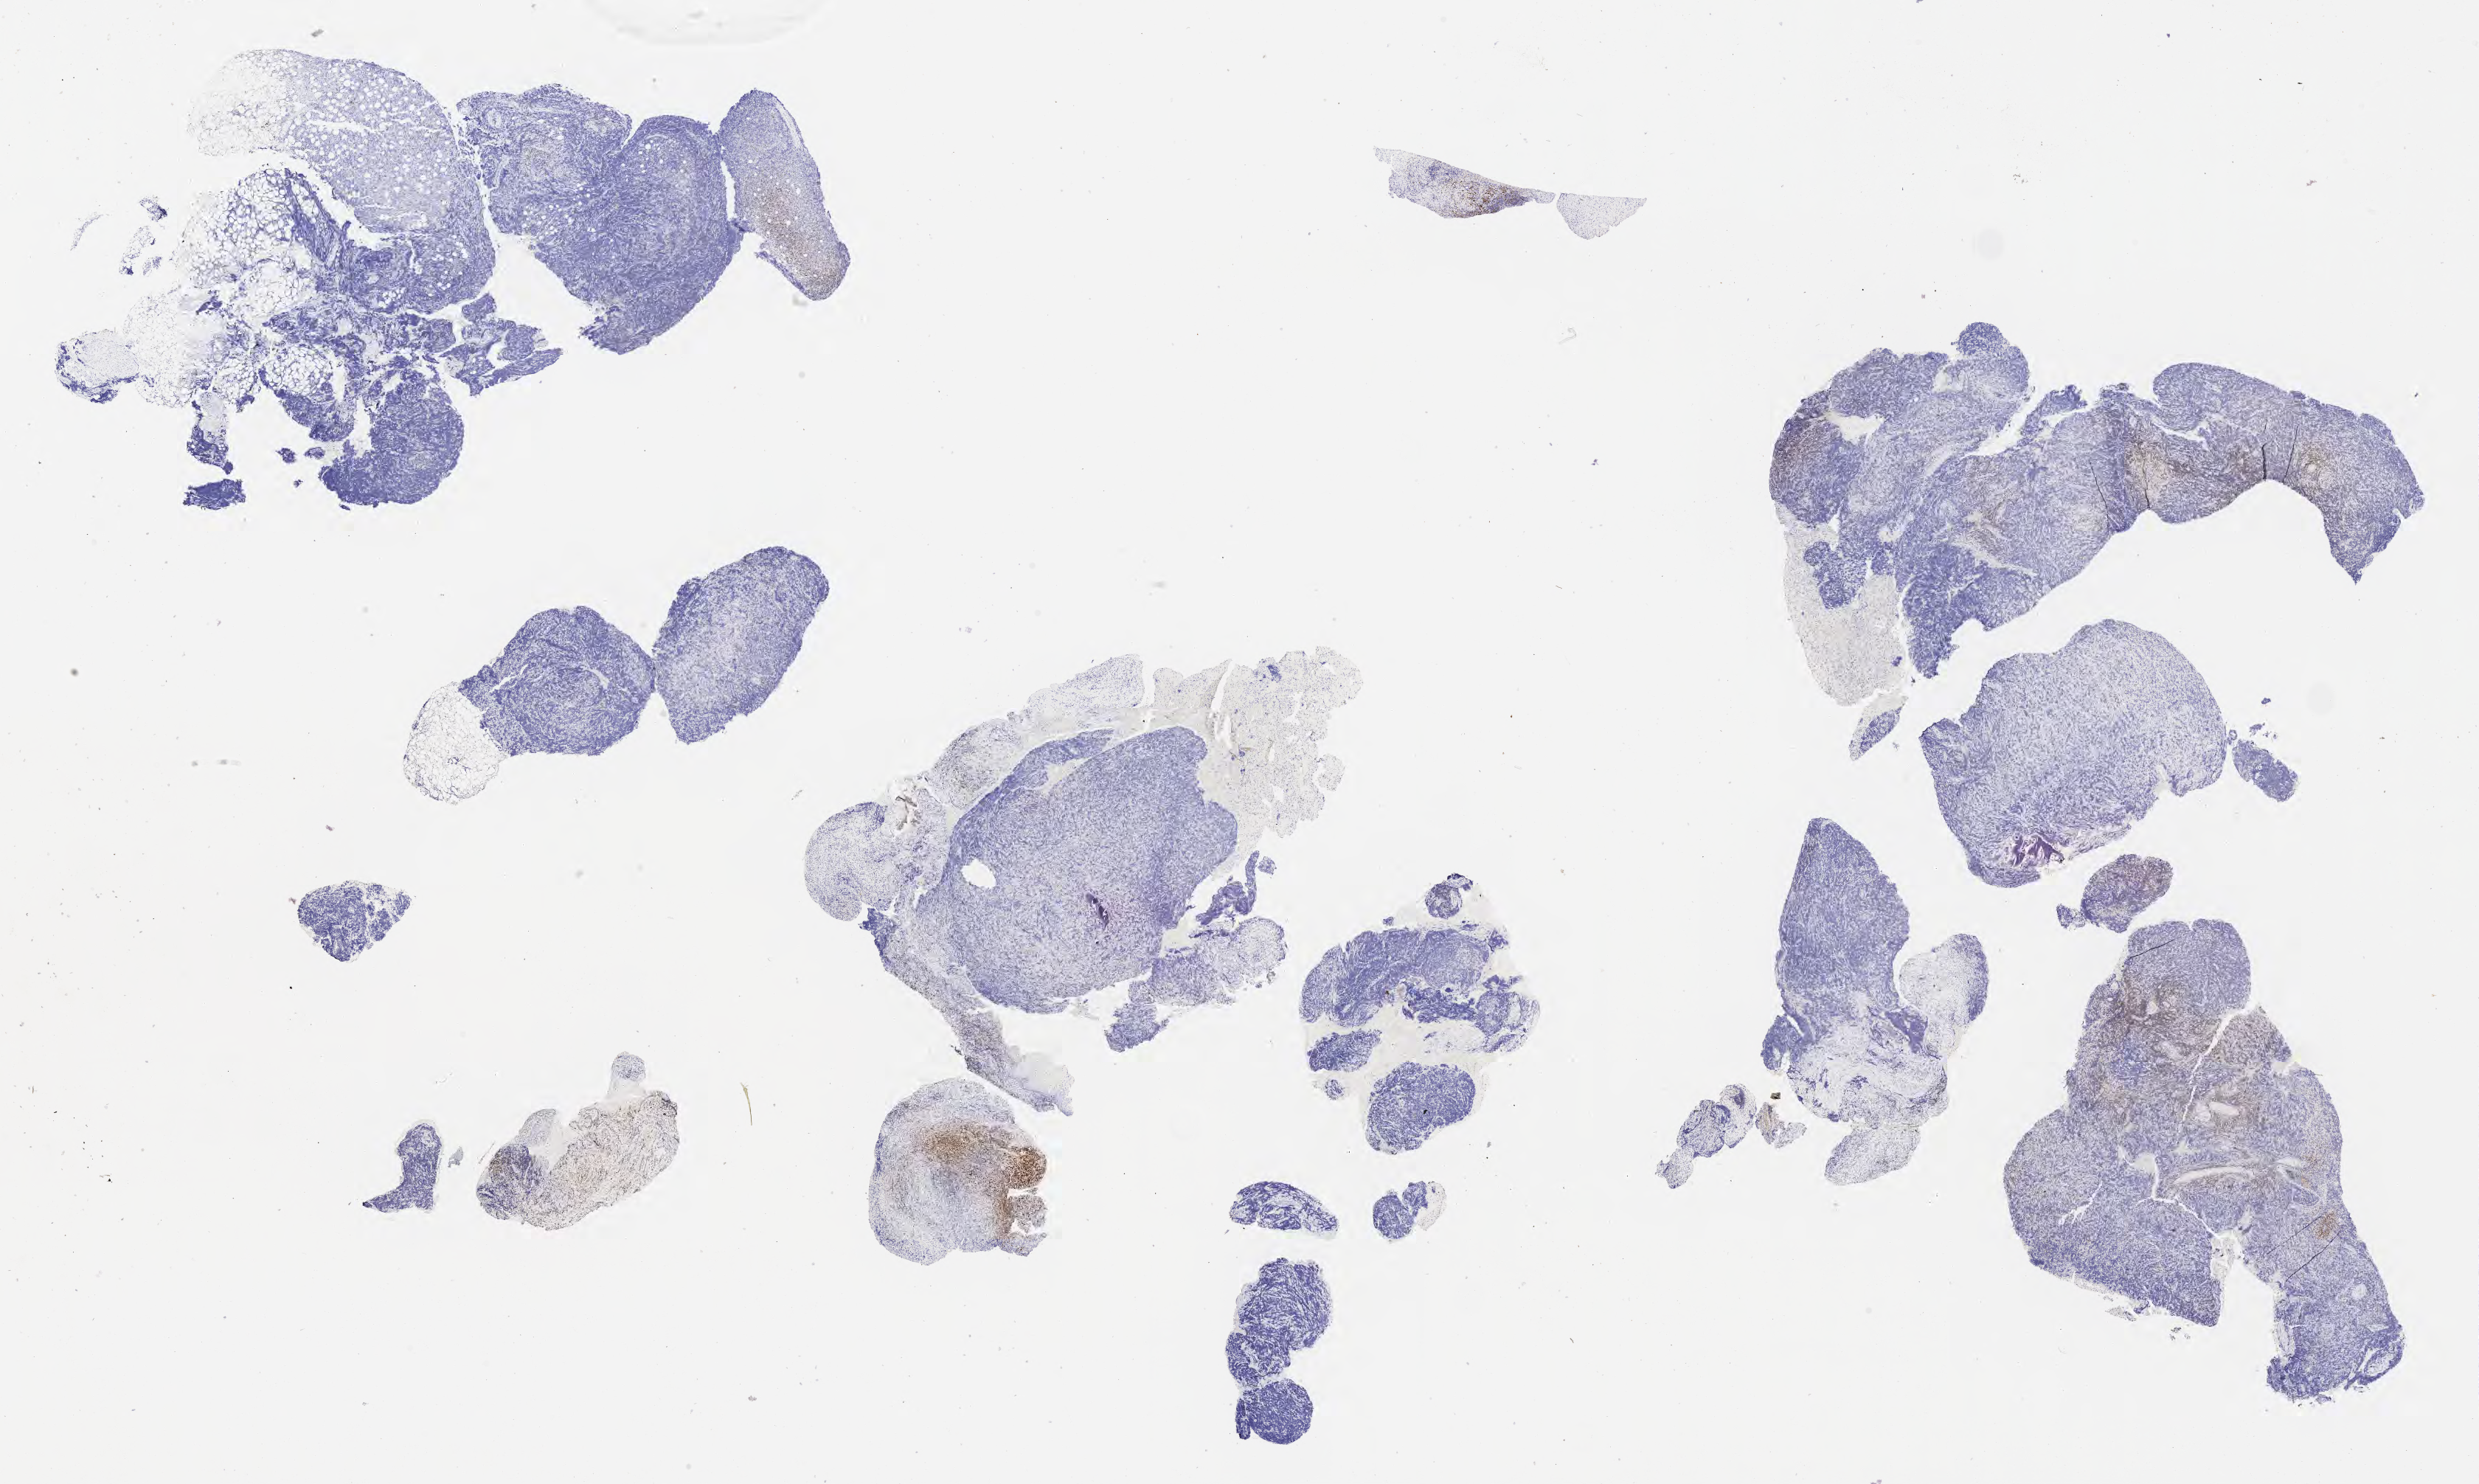
Immunohistochemistry (IHC) whole-slide image stained for IRF4/MUM1, whole scanned area (about 27.2 x 16.3 mm) shown as a low-resolution overview; tumor tissue. Male patient, 45 years old.
Histologic diagnosis: Diffuse large B-cell lymphoma, NOS.